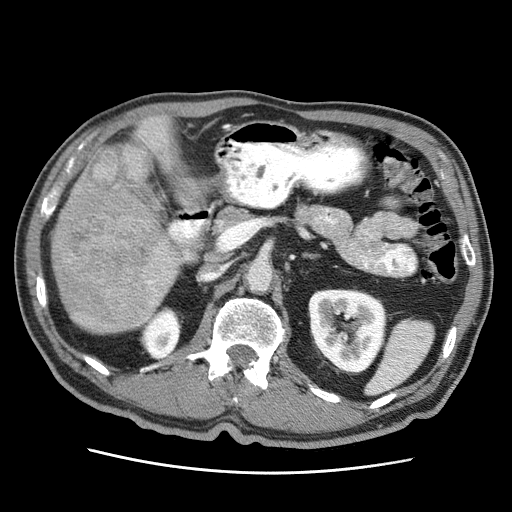
Contrast-enhanced abdominal CT (liver protocol), one axial slice; slice 17 of 75 in the series (ordered by position); 120 kVp; soft-tissue window (W 400 / L 40 HU); 512 × 512 image matrix, field of view 360 × 360 mm. Case-level facts recorded for this patient, not image findings: diagnosis: hepatocellular carcinoma (patient treated with transarterial chemoembolisation; whether this scan precedes or follows treatment is not stated here); TNM stage (as recorded): Stage-IIIA; Child-Pugh class: A; tumour differentiation: well differentiated; tumour nodularity: multinodular.
Structures marked on this image (semi-automatically segmented with operator editing):
- liver parenchyma outside the tumour (the mass and vessels are separate outlines, so this box may not span the whole liver): box from (x=52, y=115) to (x=180, y=332) px
- mass: (x=53, y=147)–(x=156, y=324)
- liver vessels: (x=153, y=289)–(x=156, y=291)